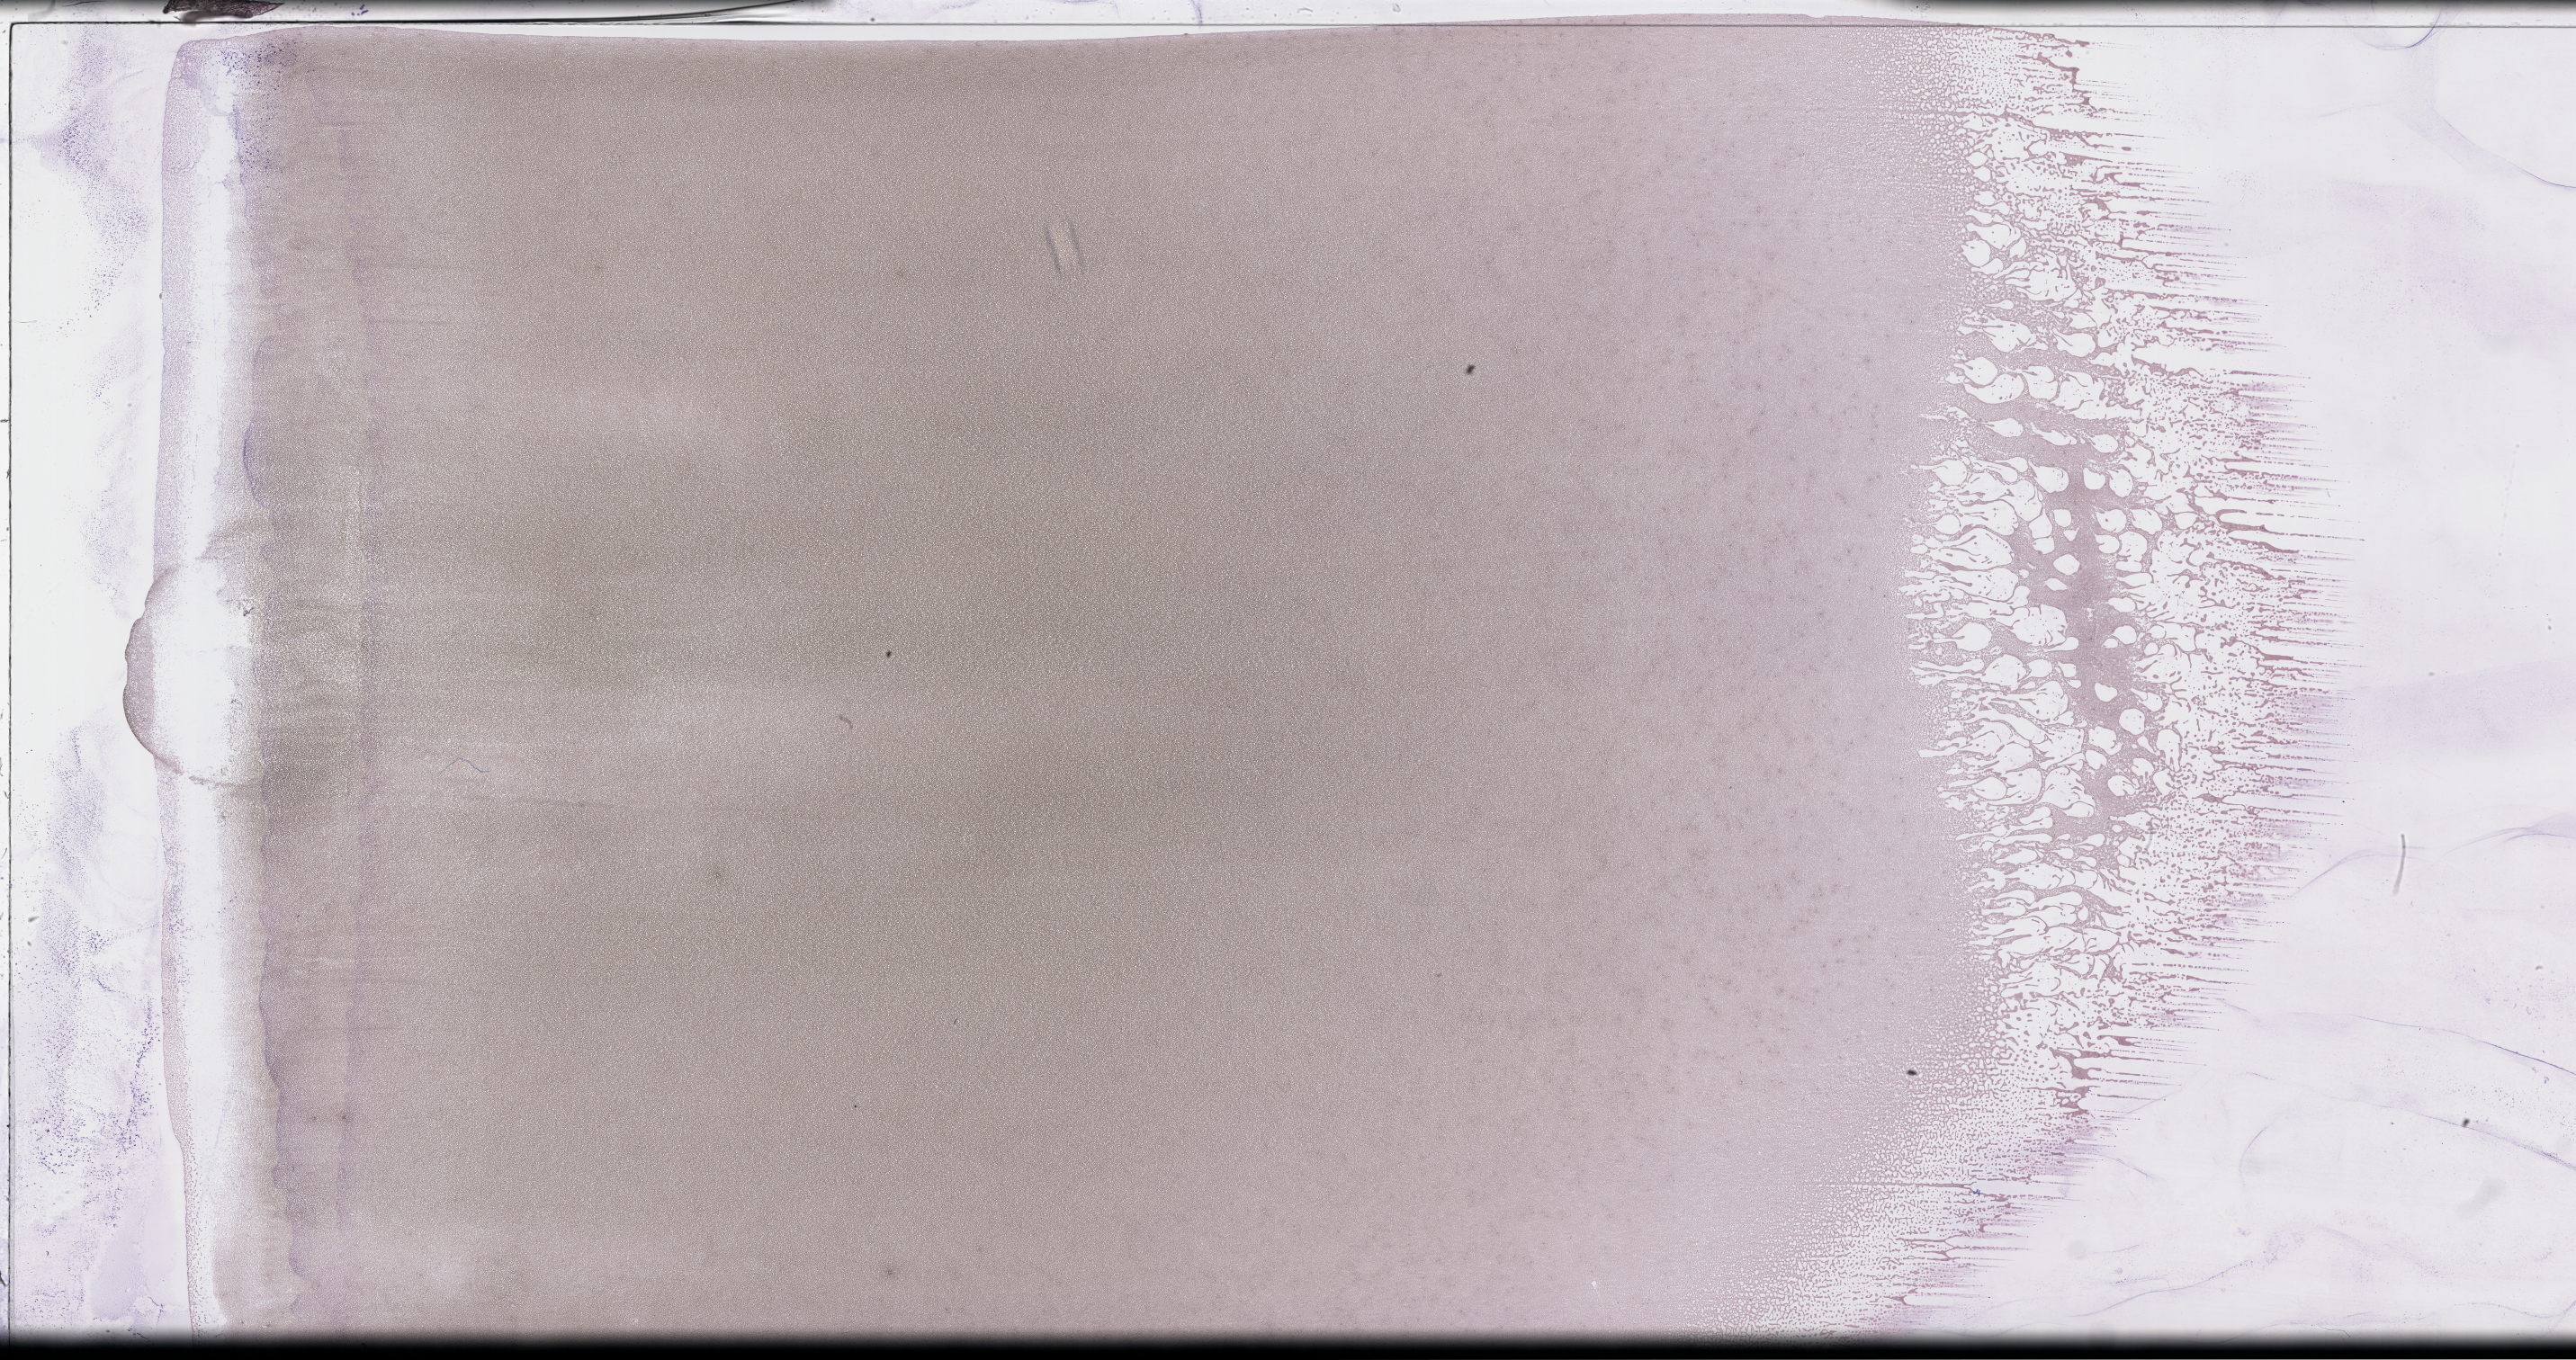
Whole-slide image of a whole blood smear, Wright–Giemsa stain — shown as a low-resolution overview of the whole scanned area (about 46.2 x 24.4 mm), collected on treatment. Patient: male.
From a patient with: Plasma Cell Myeloma.